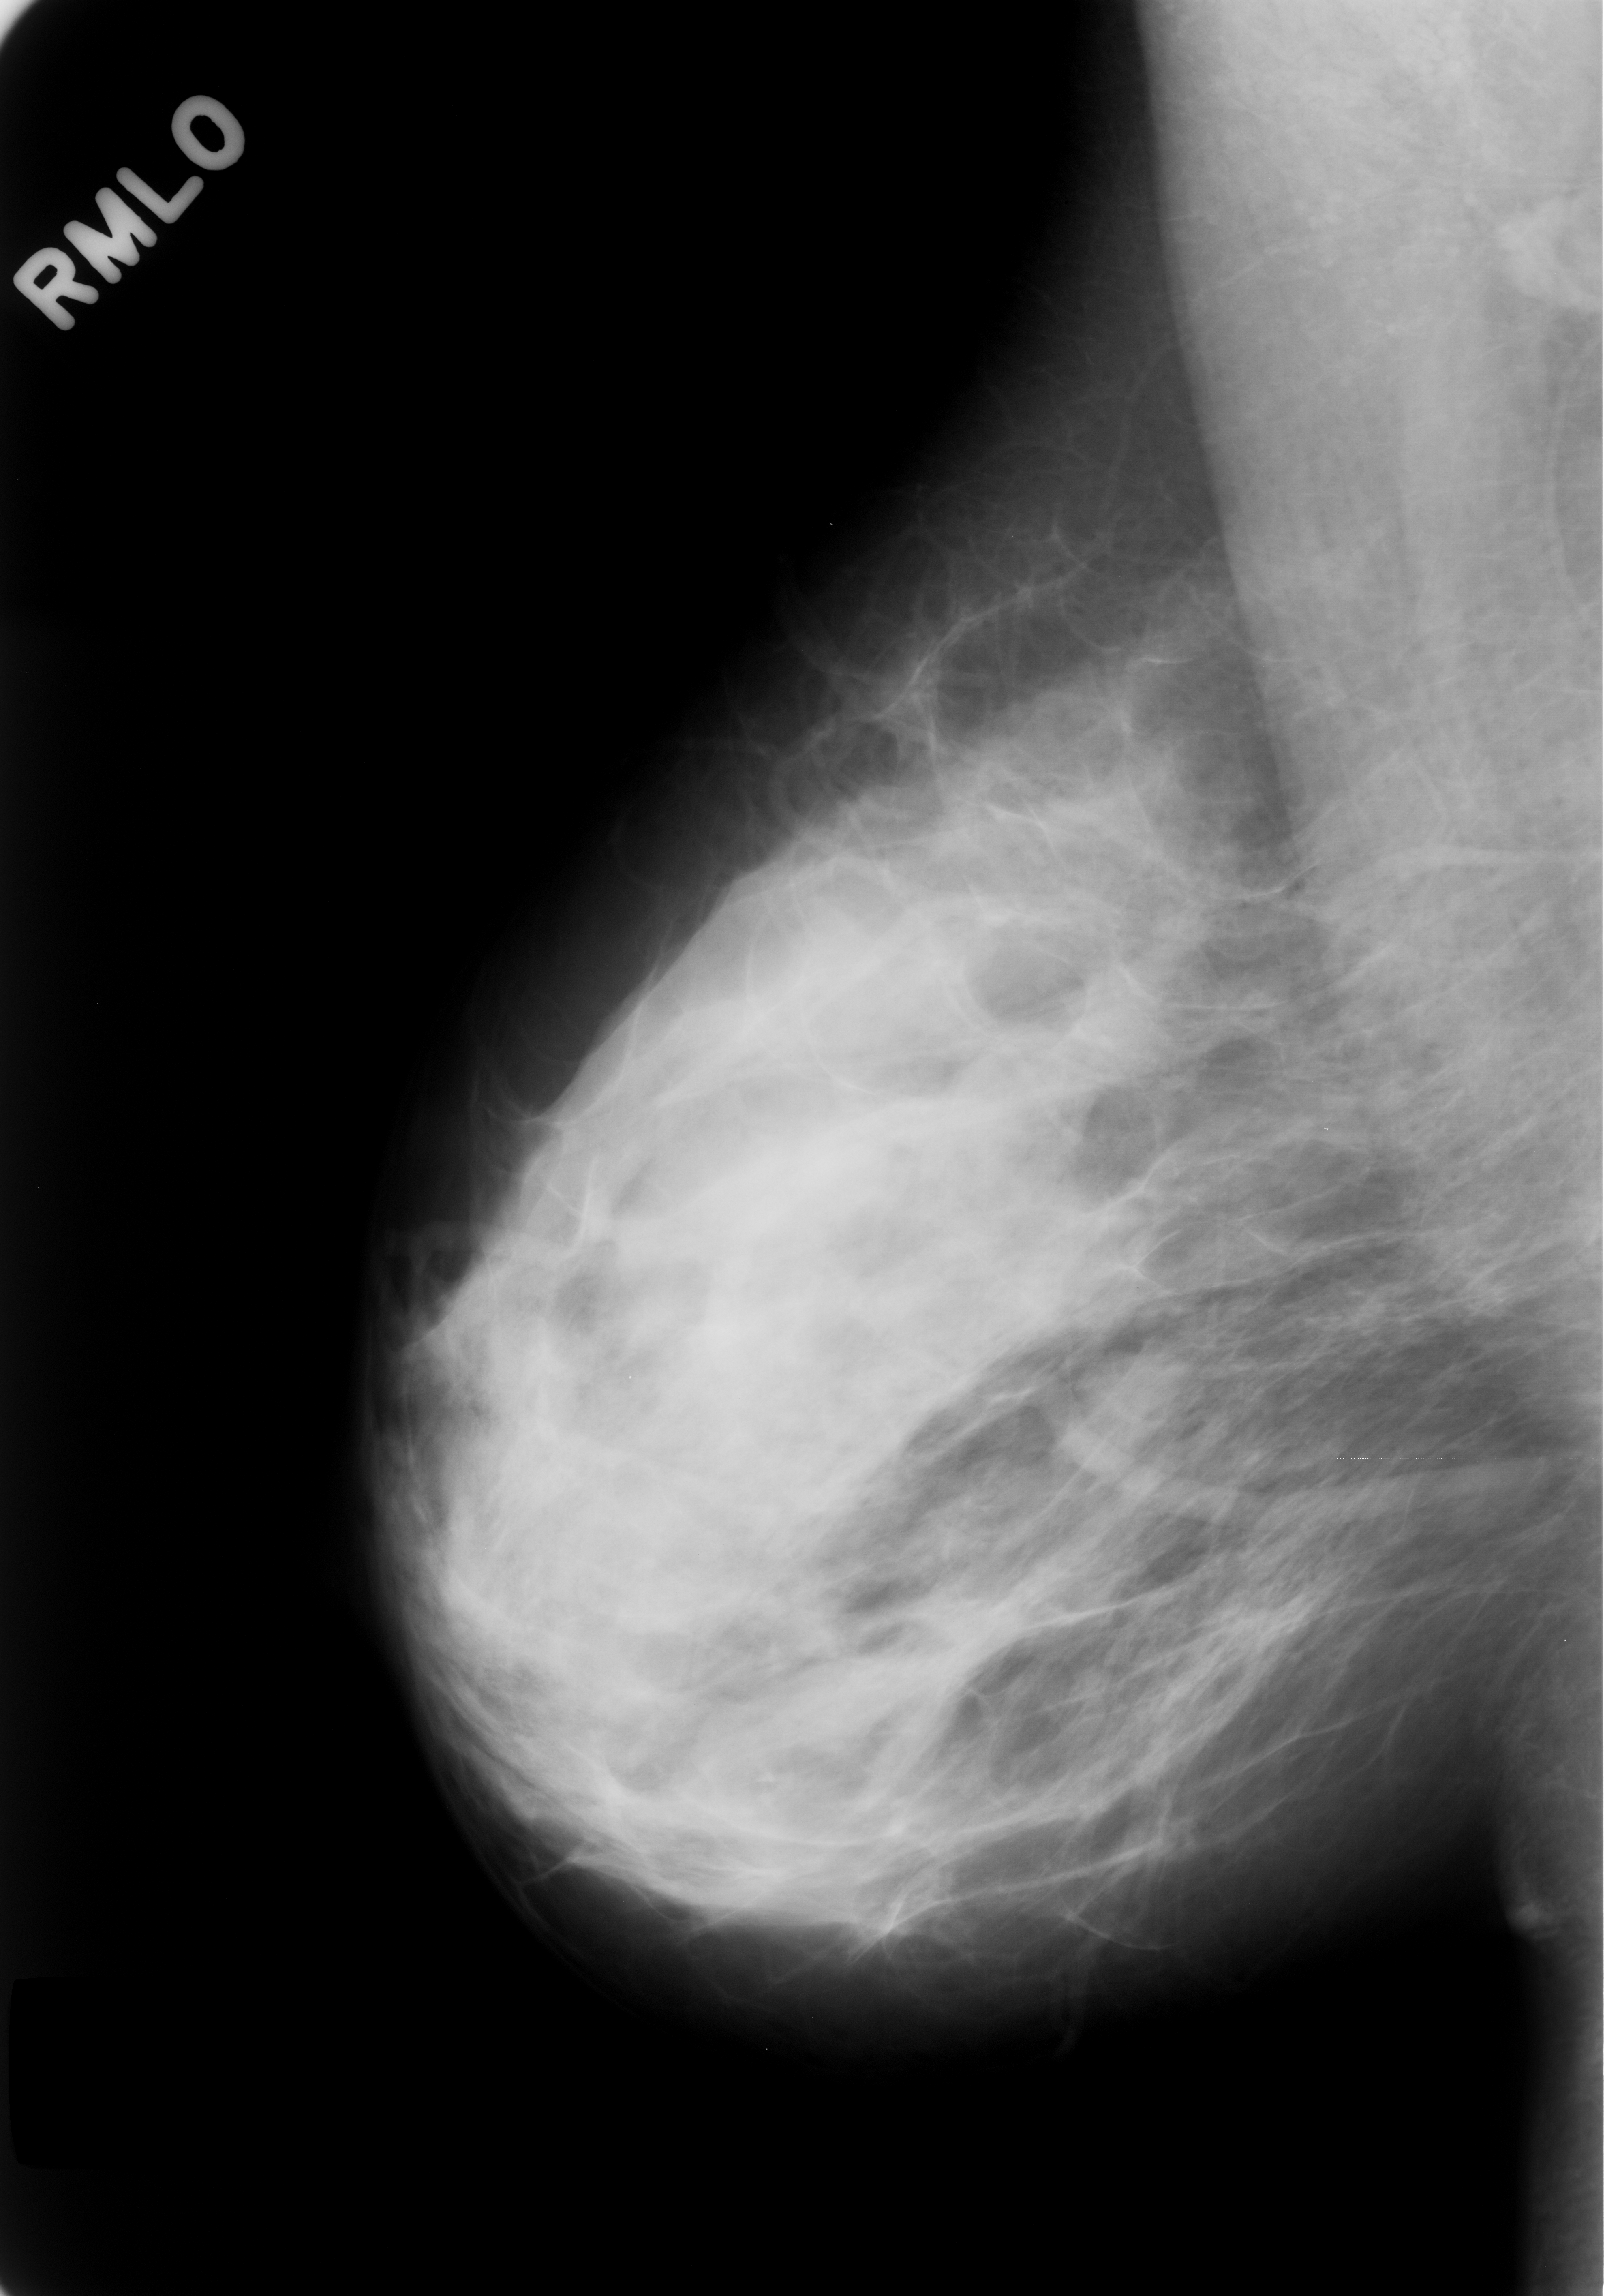
Digitized screen-film mammogram; right breast; MLO view; 1605 × 2296 image matrix.
Expert-marked regions of interest on this image (one box per marked abnormality):
- mass, shape lobulated, margins obscured; BI-RADS assessment category 3; benign; no additional work-up was recommended (outcome (as recorded, no biopsy): benign without callback): bounding box (x1, y1, x2, y2) in pixels: (1055, 1306, 1201, 1462)